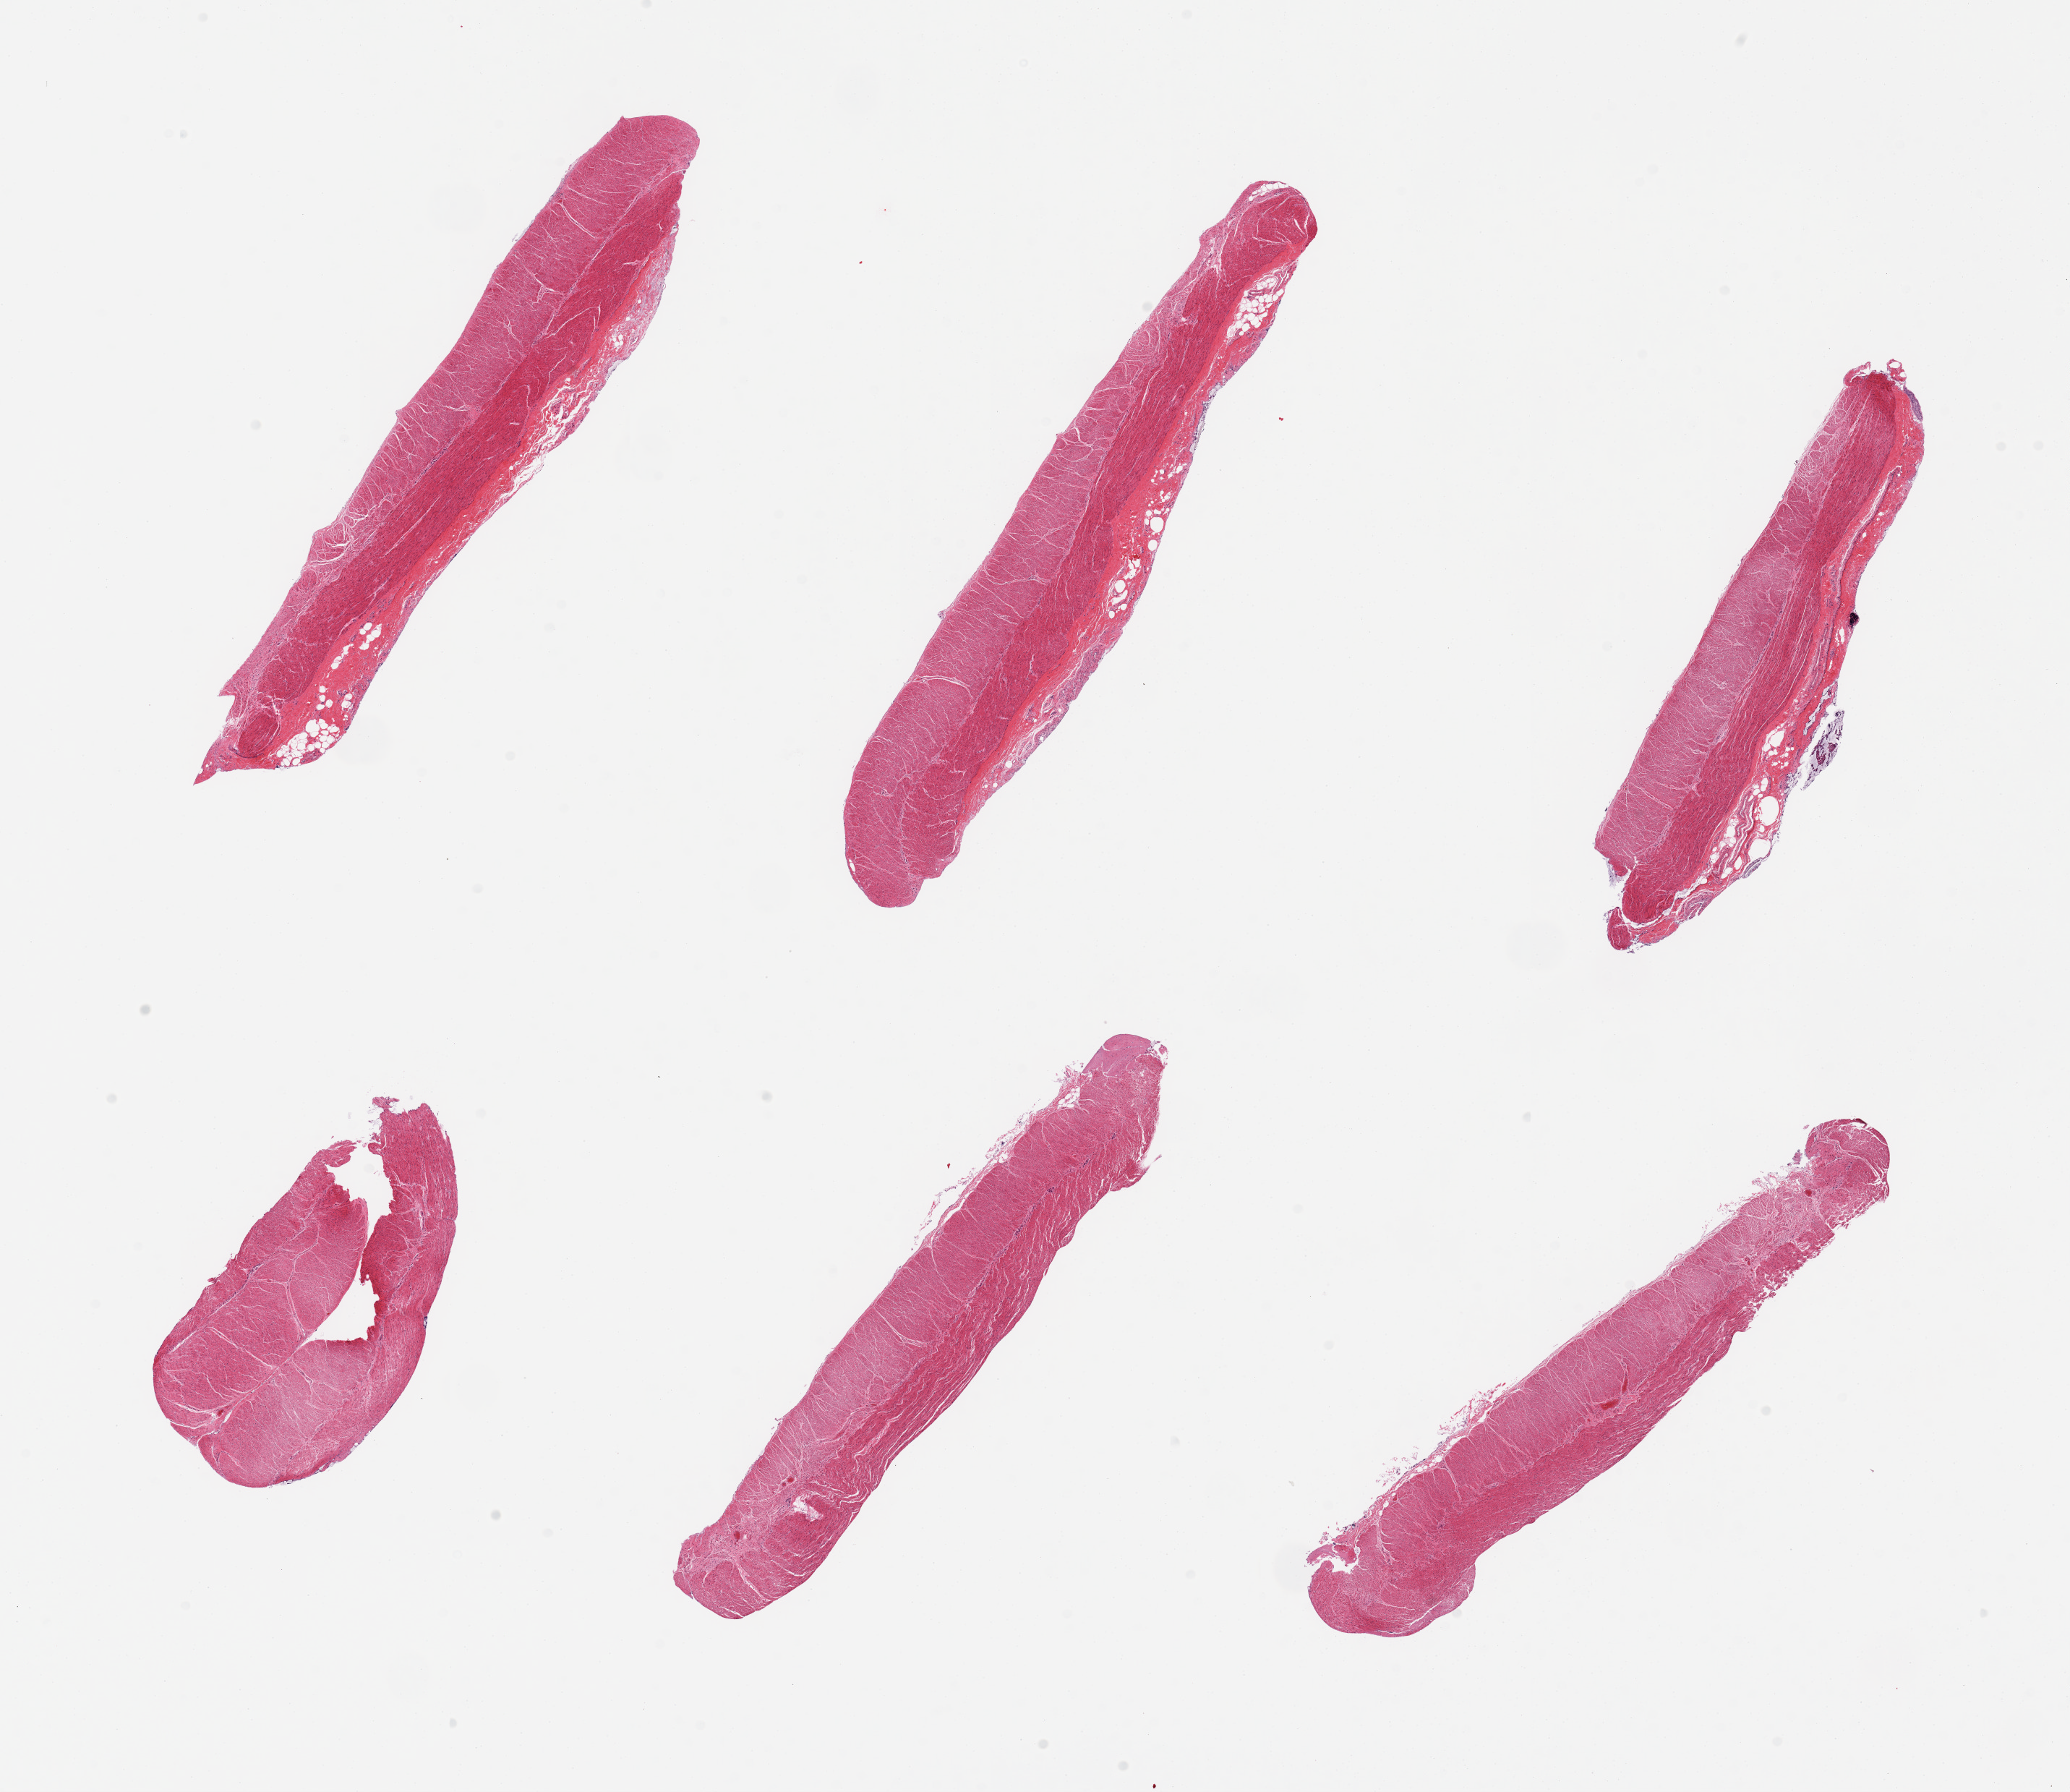
Whole-slide image, haematoxylin and eosin stain, whole scanned area (about 22.6 x 19.6 mm) shown as a low-resolution overview, PAXgene-fixed, paraffin-embedded tissue, section of sigmoid colon (target tissue), tissue donor sample. Male donor.
Reviewer comment on this tissue sample: 6 pieces, muscularis with few remnants of autolyzed mucosa.